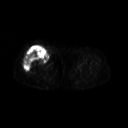
FDG PET of an extremity soft-tissue mass (from a PET/CT study), one axial slice; slice 240 of 311 in the series (ordered by position); 3.27 mm slice thickness; 128 × 128 image matrix, field of view 500 × 500 mm. Female patient, age 57 years. From the clinical record (not read from this slice): histological type: pleiomorphic undifferentiated sarcoma; grade: high; site of the primary tumour: right quadricep.
Structures marked on this image (expert contour drawn on MRI and transferred to this co-registered scan by the dataset authors):
- tumour plus oedema (research contour): bounding box (x1, y1, x2, y2) in pixels: (24, 47, 47, 71)
- tumour (research contour): (24, 47, 47, 71)